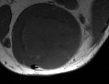
MRI of an extremity soft-tissue mass, one axial slice; slice 32 of 50 in the series (ordered by position); MR volume resampled by the dataset authors to the PET/CT grid (not the native acquisition matrix); 3.27 mm slice thickness; 109 × 84 image matrix, field of view 106 × 82 mm. Male patient. Case-level facts recorded for this patient, not image findings: histological type: synovial sarcoma; site of the primary tumour: left poplietal fossa.
Structures marked on this image (expert contour drawn on MRI and transferred to this co-registered scan by the dataset authors):
- gross tumour volume (mass): bounding box <18,16,81,68> (left, top, right, bottom; pixels)